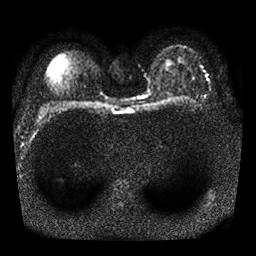
Breast MRI, one axial slice. Slice 20 of 25 in the series (ordered by position). Diffusion-weighted series; image 2 of 4 stored at this slice position (different b-values; order by instance number). 1.5 T. 4 mm slice thickness. 256 × 256 image matrix, field of view 310 × 310 mm. Female patient.
Annotated regions visible in this slice (manually delineated by an expert):
- tumour on diffusion-weighted imaging: box from (x=167, y=92) to (x=170, y=96) px